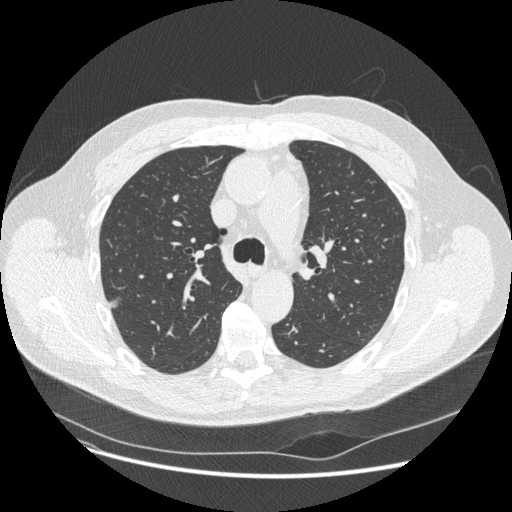
Chest CT (low-dose screening protocol), one axial image. Second screening round (one year after baseline). Lung window (W 1500 / L -600 HU). 1.25 mm slice thickness. Standard (soft-tissue) reconstruction kernel (STANDARD). 120 kVp. Male, age 62 years at enrolment. Current smoker at enrolment.
• Expert-annotated lung lesion, bounding box (x1, y1, x2, y2) in pixels: (100, 292, 128, 318).
• Screening reader's record for this exam (one nodule recorded; not confirmed to be the boxed lesion): non-calcified nodule or mass ≥4 mm, right upper lobe, 11 × 7 mm, smooth margins, pre-existing on the prior screen: yes.
• Lung cancer was diagnosed 482 days after this screen (after the third annual screen): adenocarcinoma, NOS, right upper lobe, moderately differentiated (G2), stage IA (AJCC 6th edition), 12 mm at pathology.